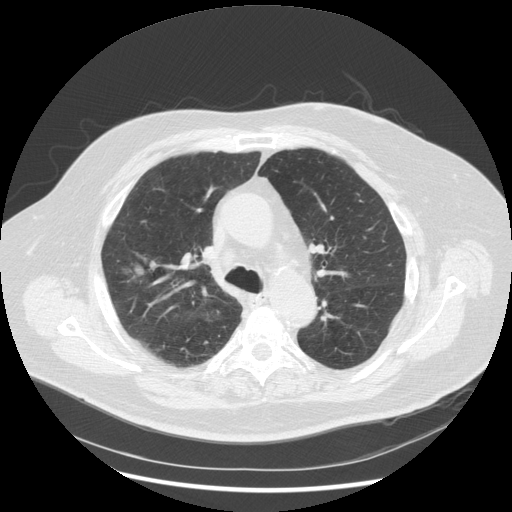
Axial slice from a low-dose chest CT screening exam, third annual screen, lung window (W 1500 / L -600 HU), 2.5 mm slice thickness, 120 kVp, slice 187 of 263 in the series, 512 × 512 image matrix. Male participant, aged 72 years at enrolment. Former smoker at enrolment.
Expert-annotated lung lesion, bounding box <98,249,156,297> (left, top, right, bottom; pixels). Reader record for this screening exam (exam-level; its link to the box is not recorded): non-calcified nodule or mass ≥4 mm, right upper lobe, 31 × 31 mm, poorly defined margins, soft tissue attenuation, pre-existing on the prior screen: no. Official screen result: positive, other. Later outcome: lung cancer diagnosed 70 days after this screen — squamous cell carcinoma, NOS, right upper lobe, poorly differentiated (G3), stage IIIA (AJCC 6th edition), 19 mm at pathology.